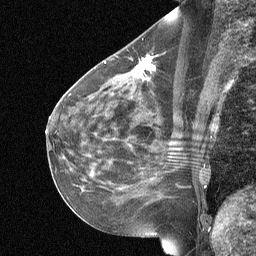
Breast MRI (dynamic contrast-enhanced), one sagittal slice. Dynamic contrast-enhanced study with each time point stored as its own series, time point 2 of 3 at this slice position (early post-contrast, ordered by acquisition time). 1.5 T. TE 4.8 ms, TR 27 ms. 256 × 256 image matrix, field of view 200 × 200 mm. Female patient, age 51 years. From the clinical record (not read from this slice): setting: breast cancer imaged before/during neoadjuvant chemotherapy; receptor status: HR-positive, HER2-negative.
Annotated regions visible in this slice (semi-automatically segmented with operator editing):
- analysis volume of interest (the breast-tissue region the enhancement analysis was run in; not a lesion): bounding box [x1, y1, x2, y2] px = [88, 42, 192, 119]
- tumour enhancement mask (voxels above the 90 % enhancement threshold inside the analysis volume of interest): [135, 56, 154, 77]